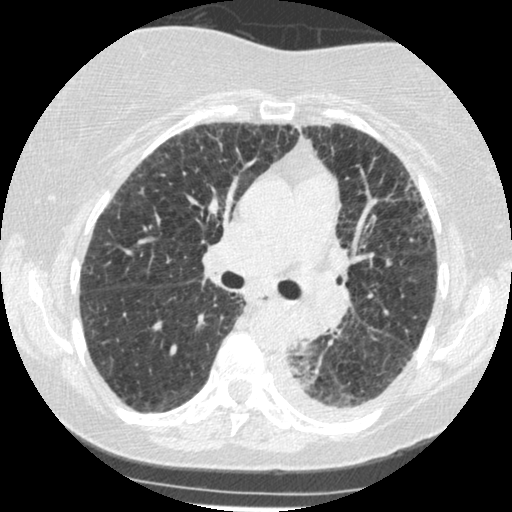
Chest CT (low-dose screening protocol), one axial image. Third annual screen. Lung window (W 1500 / L -600 HU). 120 kVp. Slice 183 of 341 in the series. Female participant, aged 60 years at enrolment. Former smoker at enrolment.
Expert-annotated lung lesion, bounding box (x1, y1, x2, y2) in pixels: (269, 308, 342, 373). Reader record for this screening exam (exam-level; its link to the box is not recorded): non-calcified nodule or mass ≥4 mm, left lower lobe, 54 × 38 mm, smooth margins, soft tissue attenuation, pre-existing on the prior screen: yes; interval growth: yes. Later outcome: lung cancer diagnosed 15 days after this screen — small cell carcinoma, NOS, left lower lobe, undifferentiated (G4), stage IV (AJCC 6th edition), 69 mm at pathology.